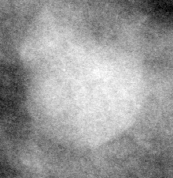
Cropped region of a digitized screen-film mammogram centred on a radiologist-marked abnormality, left breast, MLO view.
- Finding: mass, shape lobulated, margins circumscribed; BI-RADS assessment category 3; pathology result (as recorded, not read from the image): benign.